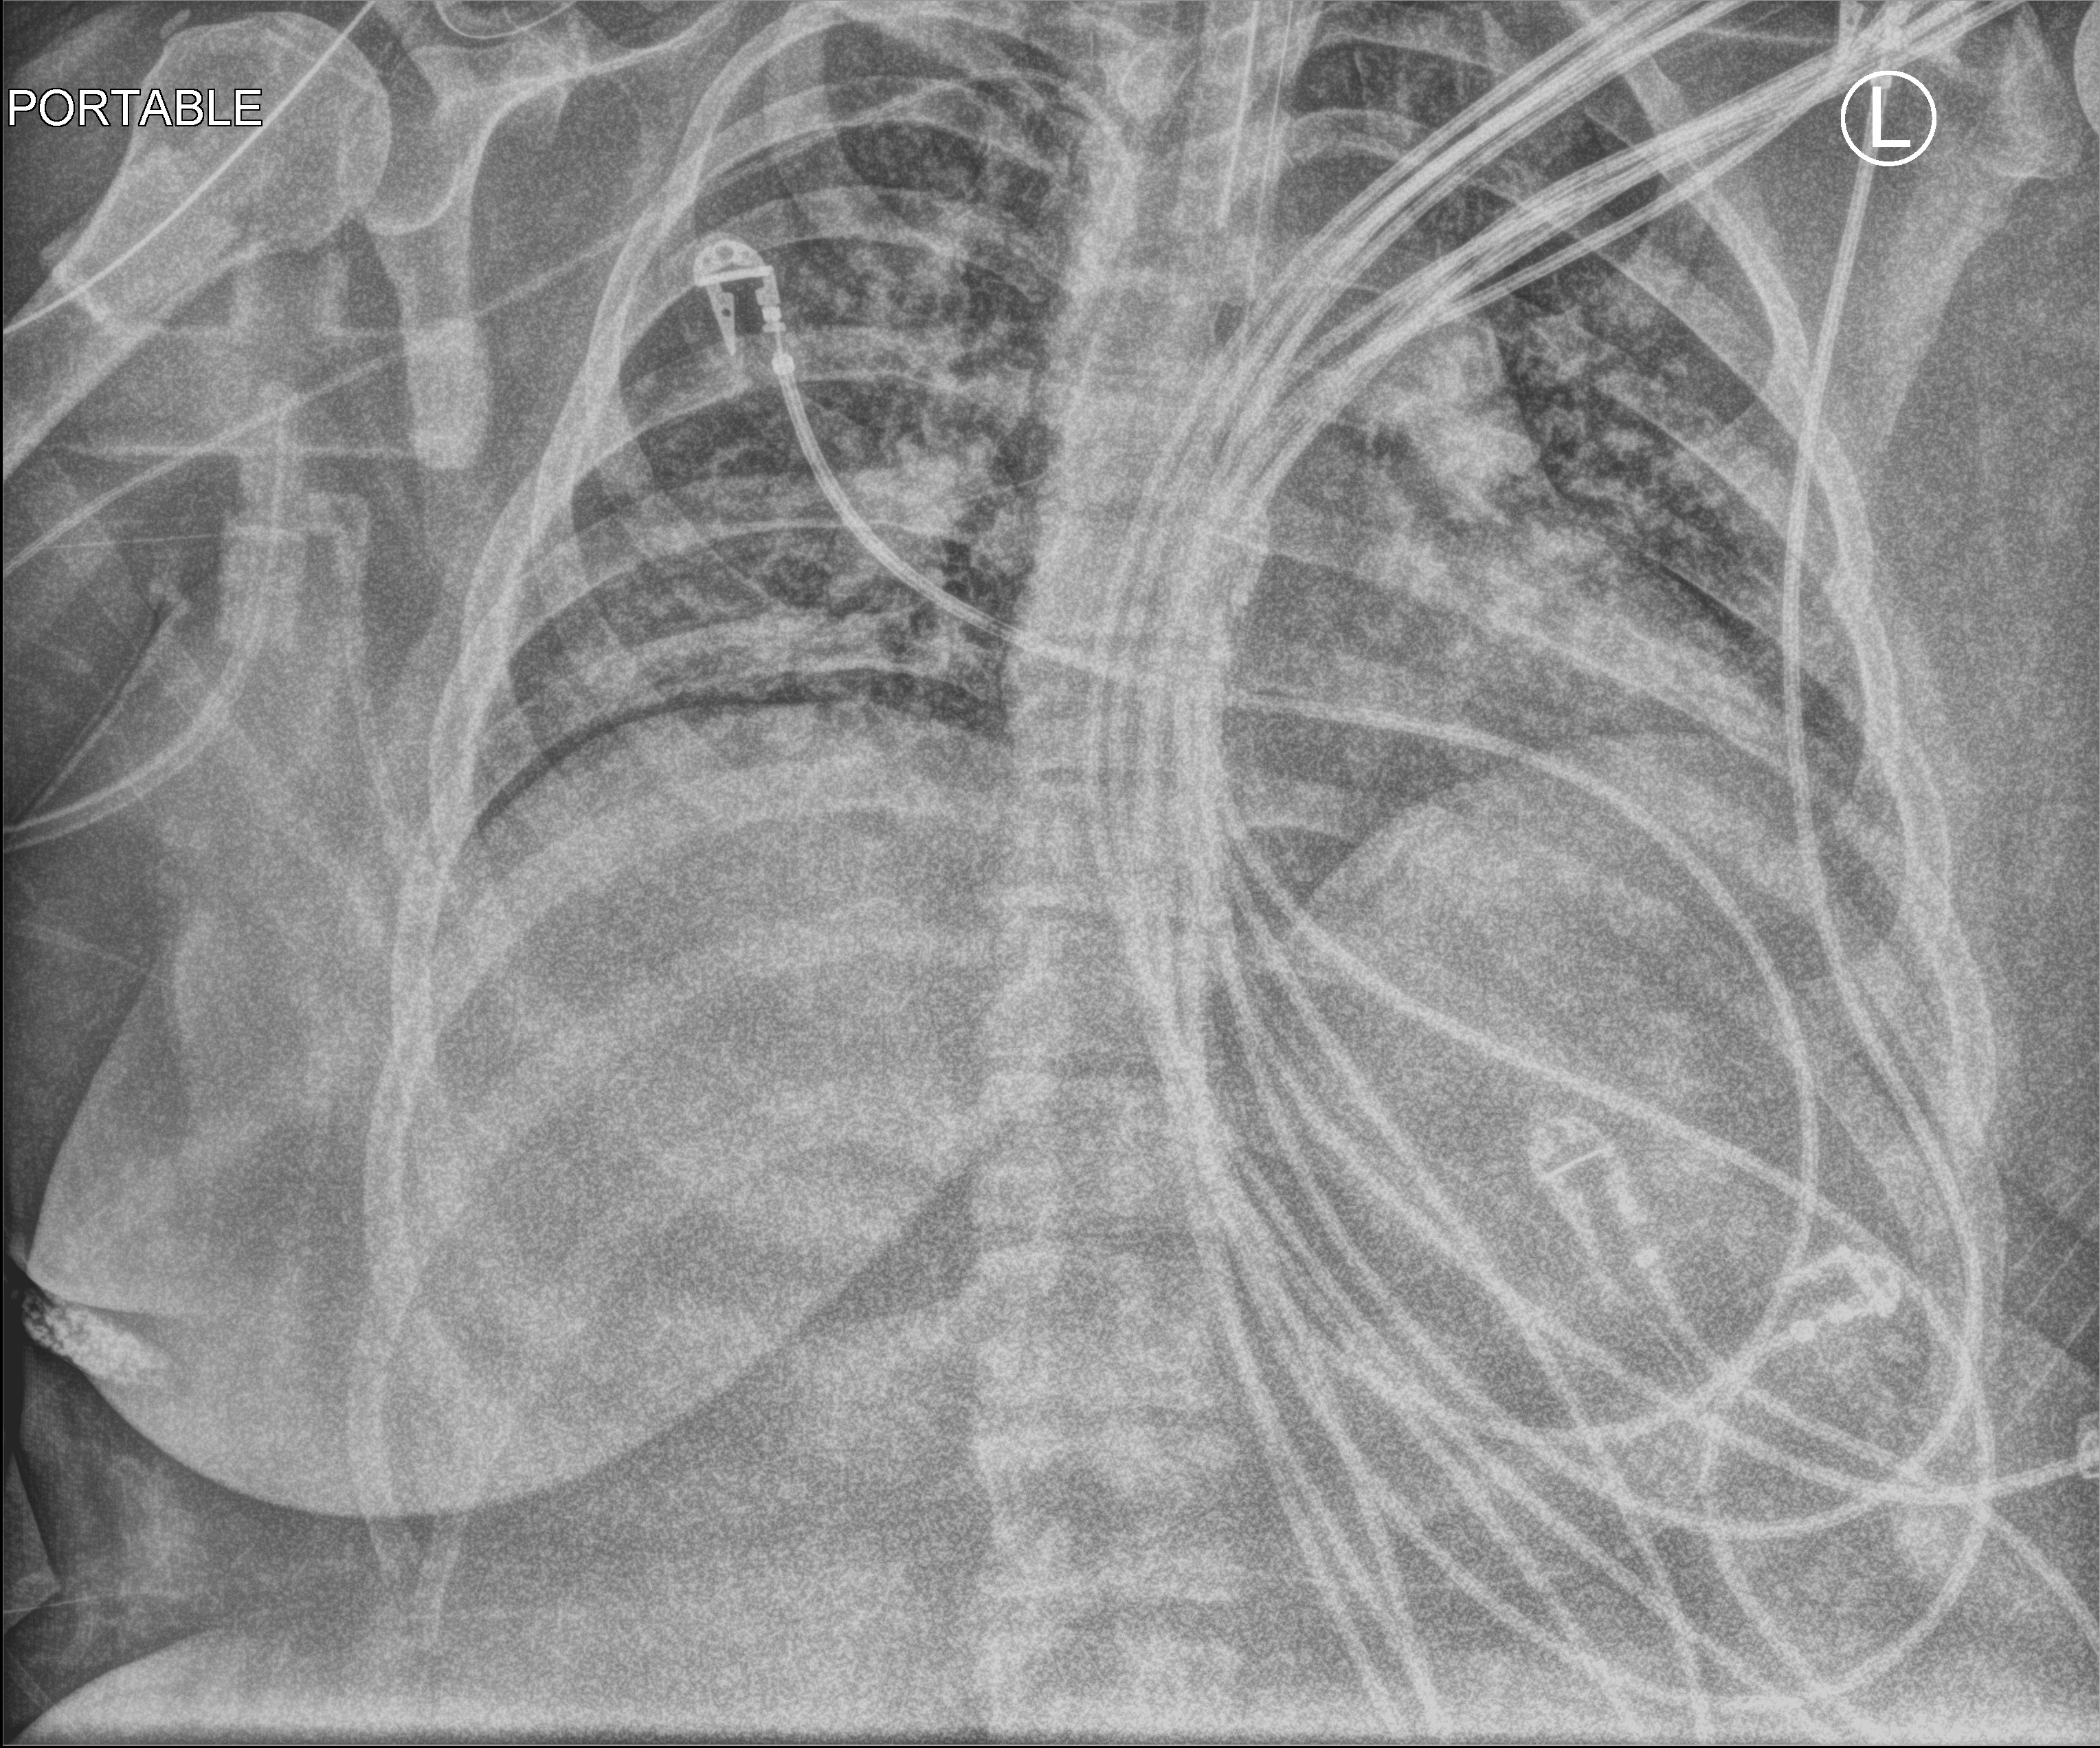
Portable chest radiograph; anteroposterior (AP) projection. Patient hospitalised with COVID-19; female, aged 18–59 years.
From the hospital-stay record, not from the radiograph (when in the stay this image was taken is not recorded):
- admitted to intensive care during this hospital stay: yes
- mechanically ventilated during this hospital stay: yes